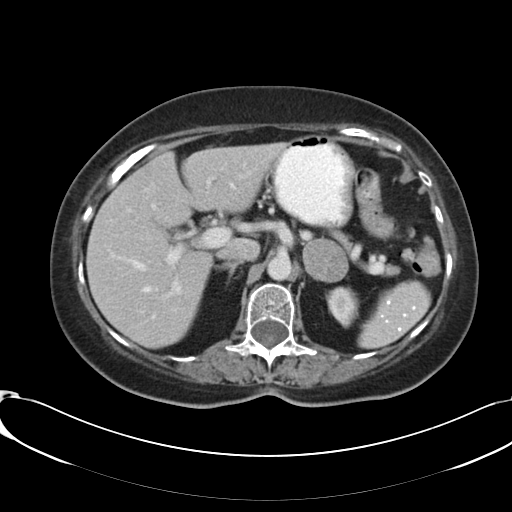
Contrast-enhanced abdominal CT, one axial slice; slice 71 of 91 in the series (ordered by position); 120 kVp; intravenous contrast given; soft-tissue window (W 400 / L 40 HU); 5 mm slice thickness; 512 × 512 image matrix, field of view 366 × 366 mm. Patient: female, 73 years. Case-level facts recorded for this patient, not image findings: diagnosis: adrenocortical carcinoma; tumour side: left adrenal; tumour size at pathology: 4.9 cm; Ki-67 index: 10 %; stage (as recorded): 3.
Outlined on this slice (semi-automatic segmentation, software-assisted and operator-edited):
- mass: bounding box (x1, y1, x2, y2) in pixels: (304, 239, 347, 280)